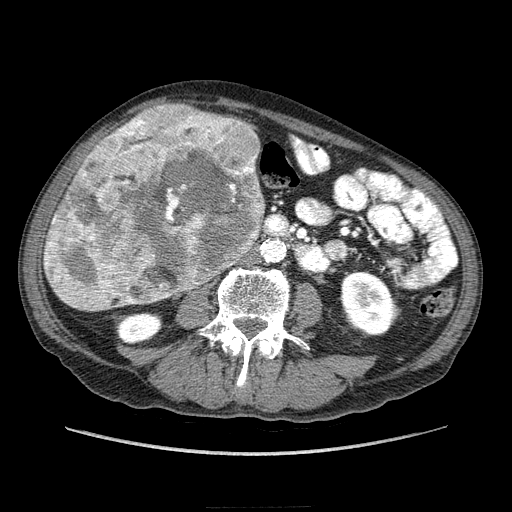
Contrast-enhanced abdominal CT (liver protocol), one axial slice. Position 65 of 218 along the scan axis. Soft-tissue window (W 400 / L 40 HU). 512 × 512 image matrix. Case-level facts recorded for this patient, not image findings: diagnosis: hepatocellular carcinoma (patient treated with transarterial chemoembolisation; whether this scan precedes or follows treatment is not stated here); TNM stage (as recorded): Stage-IIIA; Child-Pugh class: A; tumour differentiation: well differentiated; tumour nodularity: multinodular.
Structures marked on this image (semi-automatically segmented with operator editing):
- liver parenchyma outside the tumour (the mass and vessels are separate outlines, so this box may not span the whole liver): bounding box <44,136,106,270> (left, top, right, bottom; pixels)
- mass: <44,102,267,312>